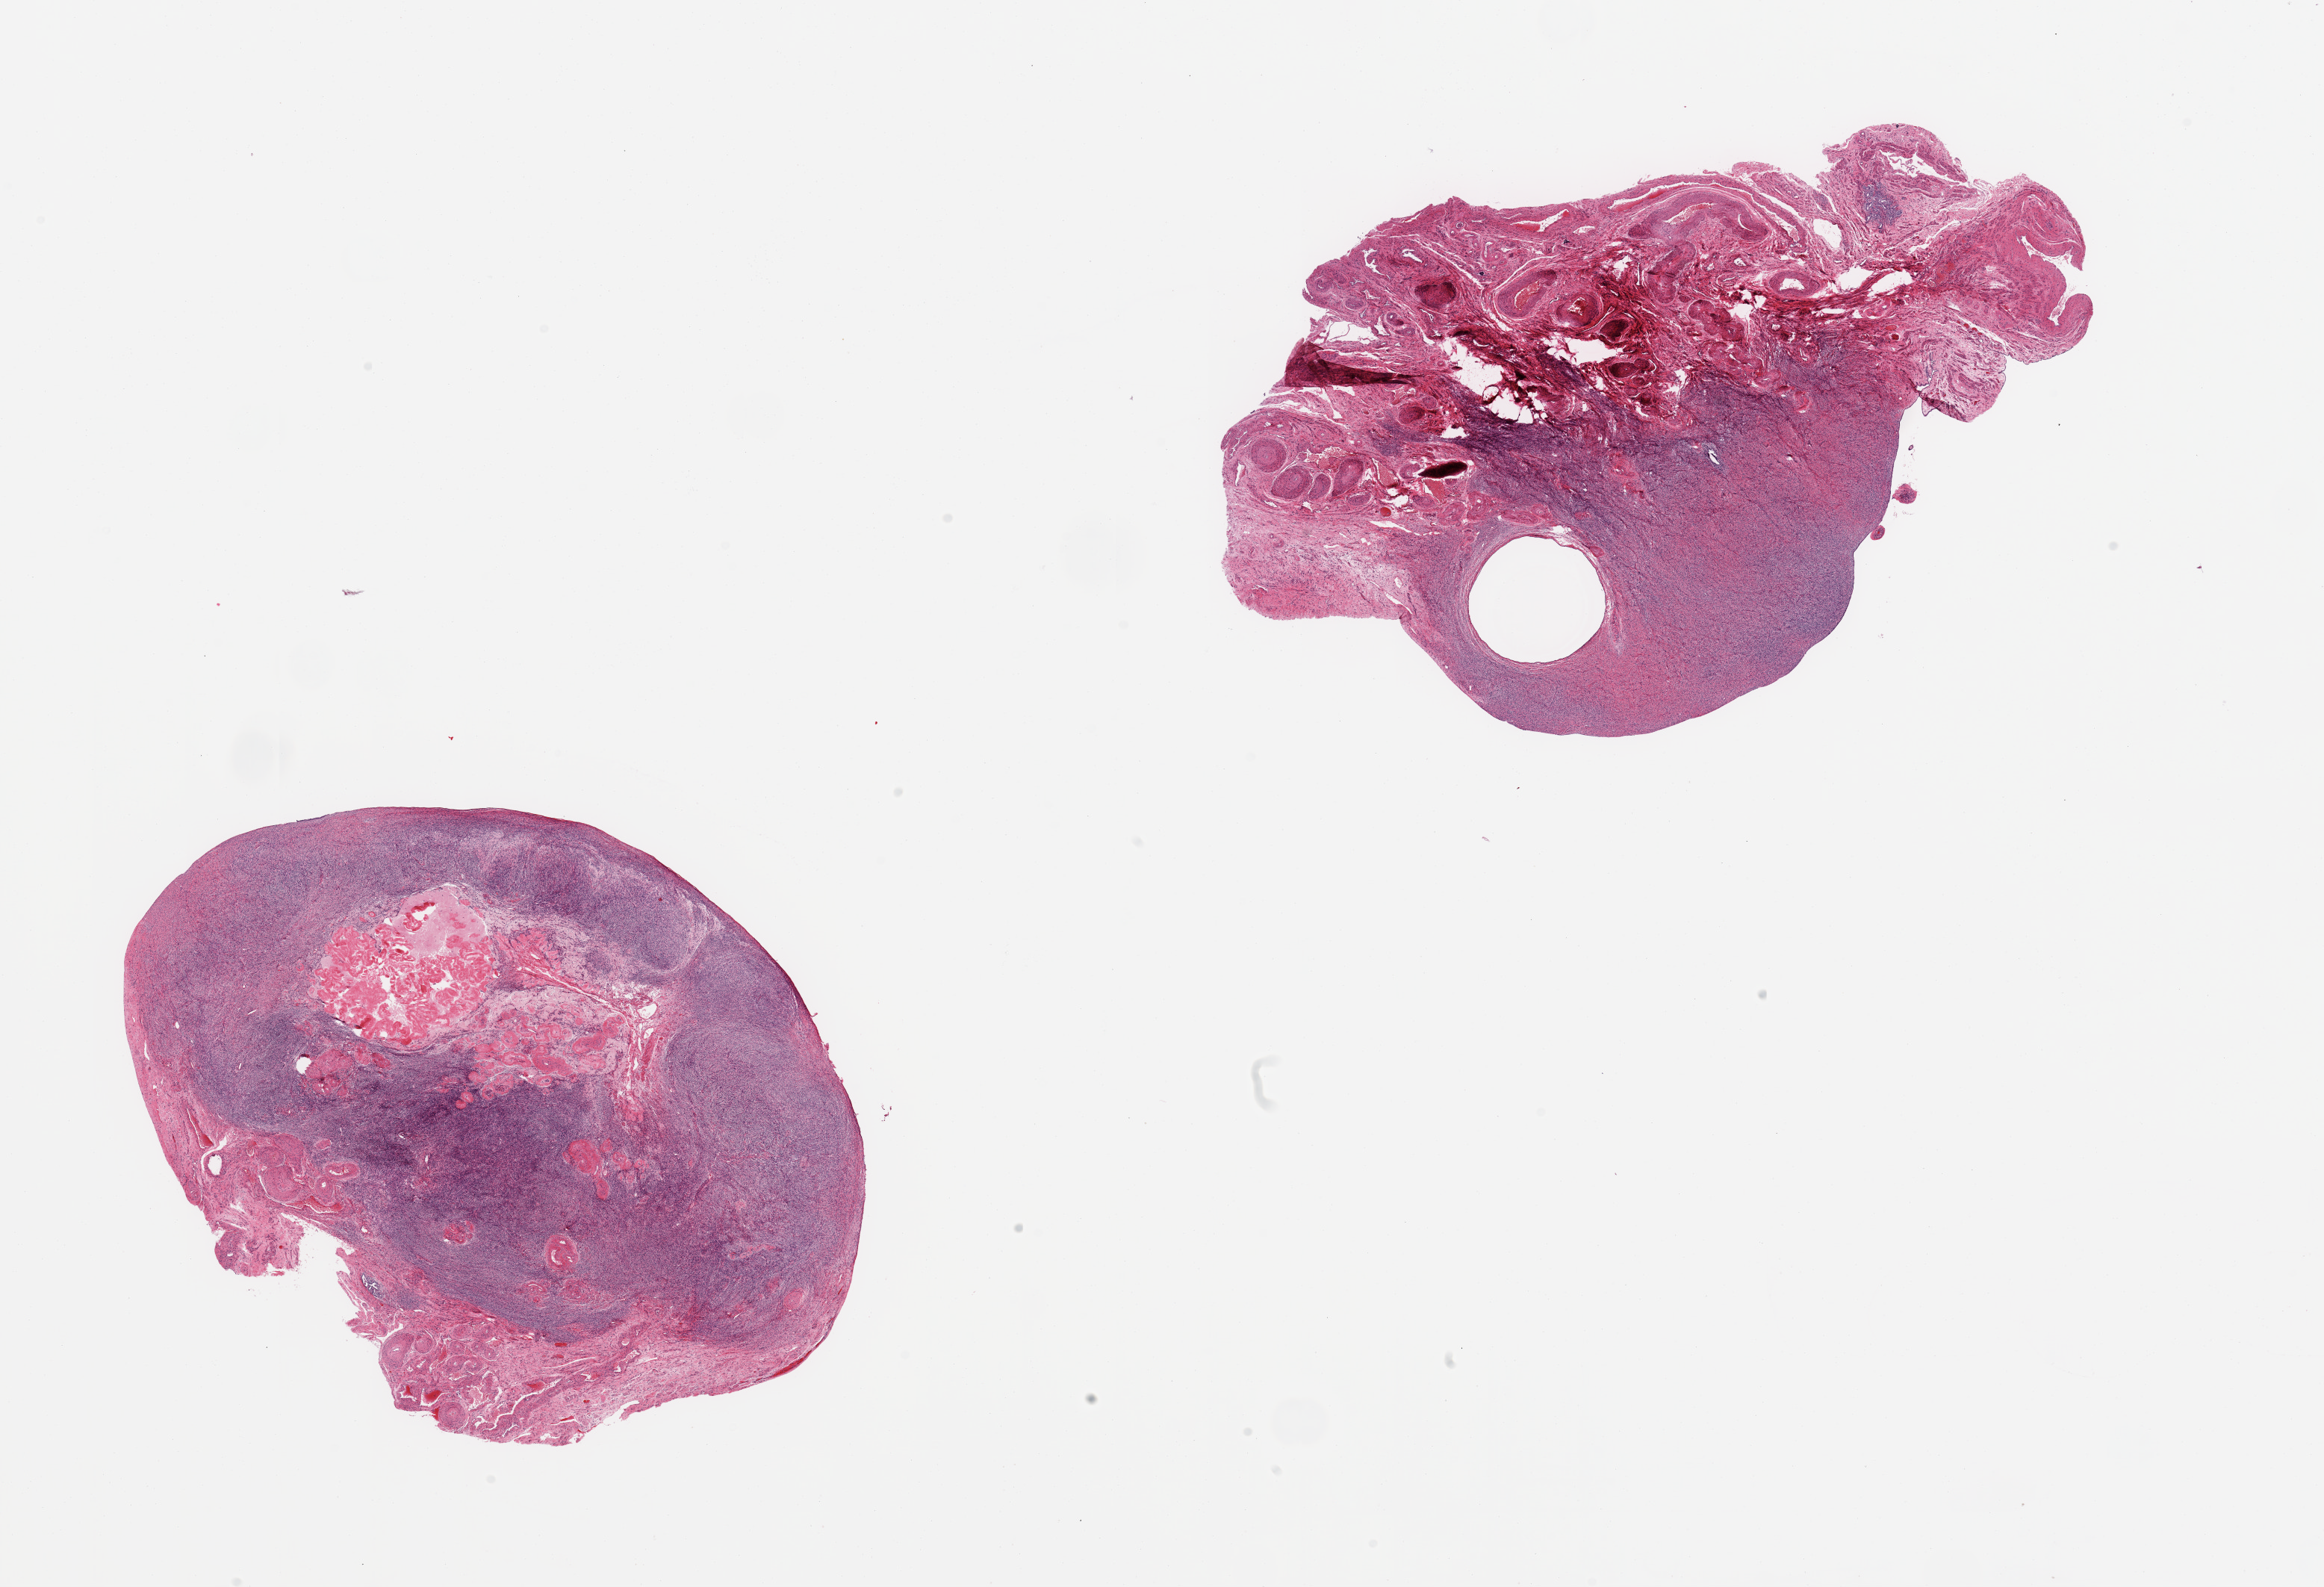
Haematoxylin and eosin whole-slide image, a low-resolution overview of the entire scanned area, about 24.6 x 16.8 mm, PAXgene-fixed paraffin-embedded (PFPE) section, section of ovary (target tissue), tissue donor sample. Donor sex: female.
Reviewer comment on this tissue sample: 2 pieces; atrophic with corpora albicantia and a small cyst; high vascular content in 1 piece.